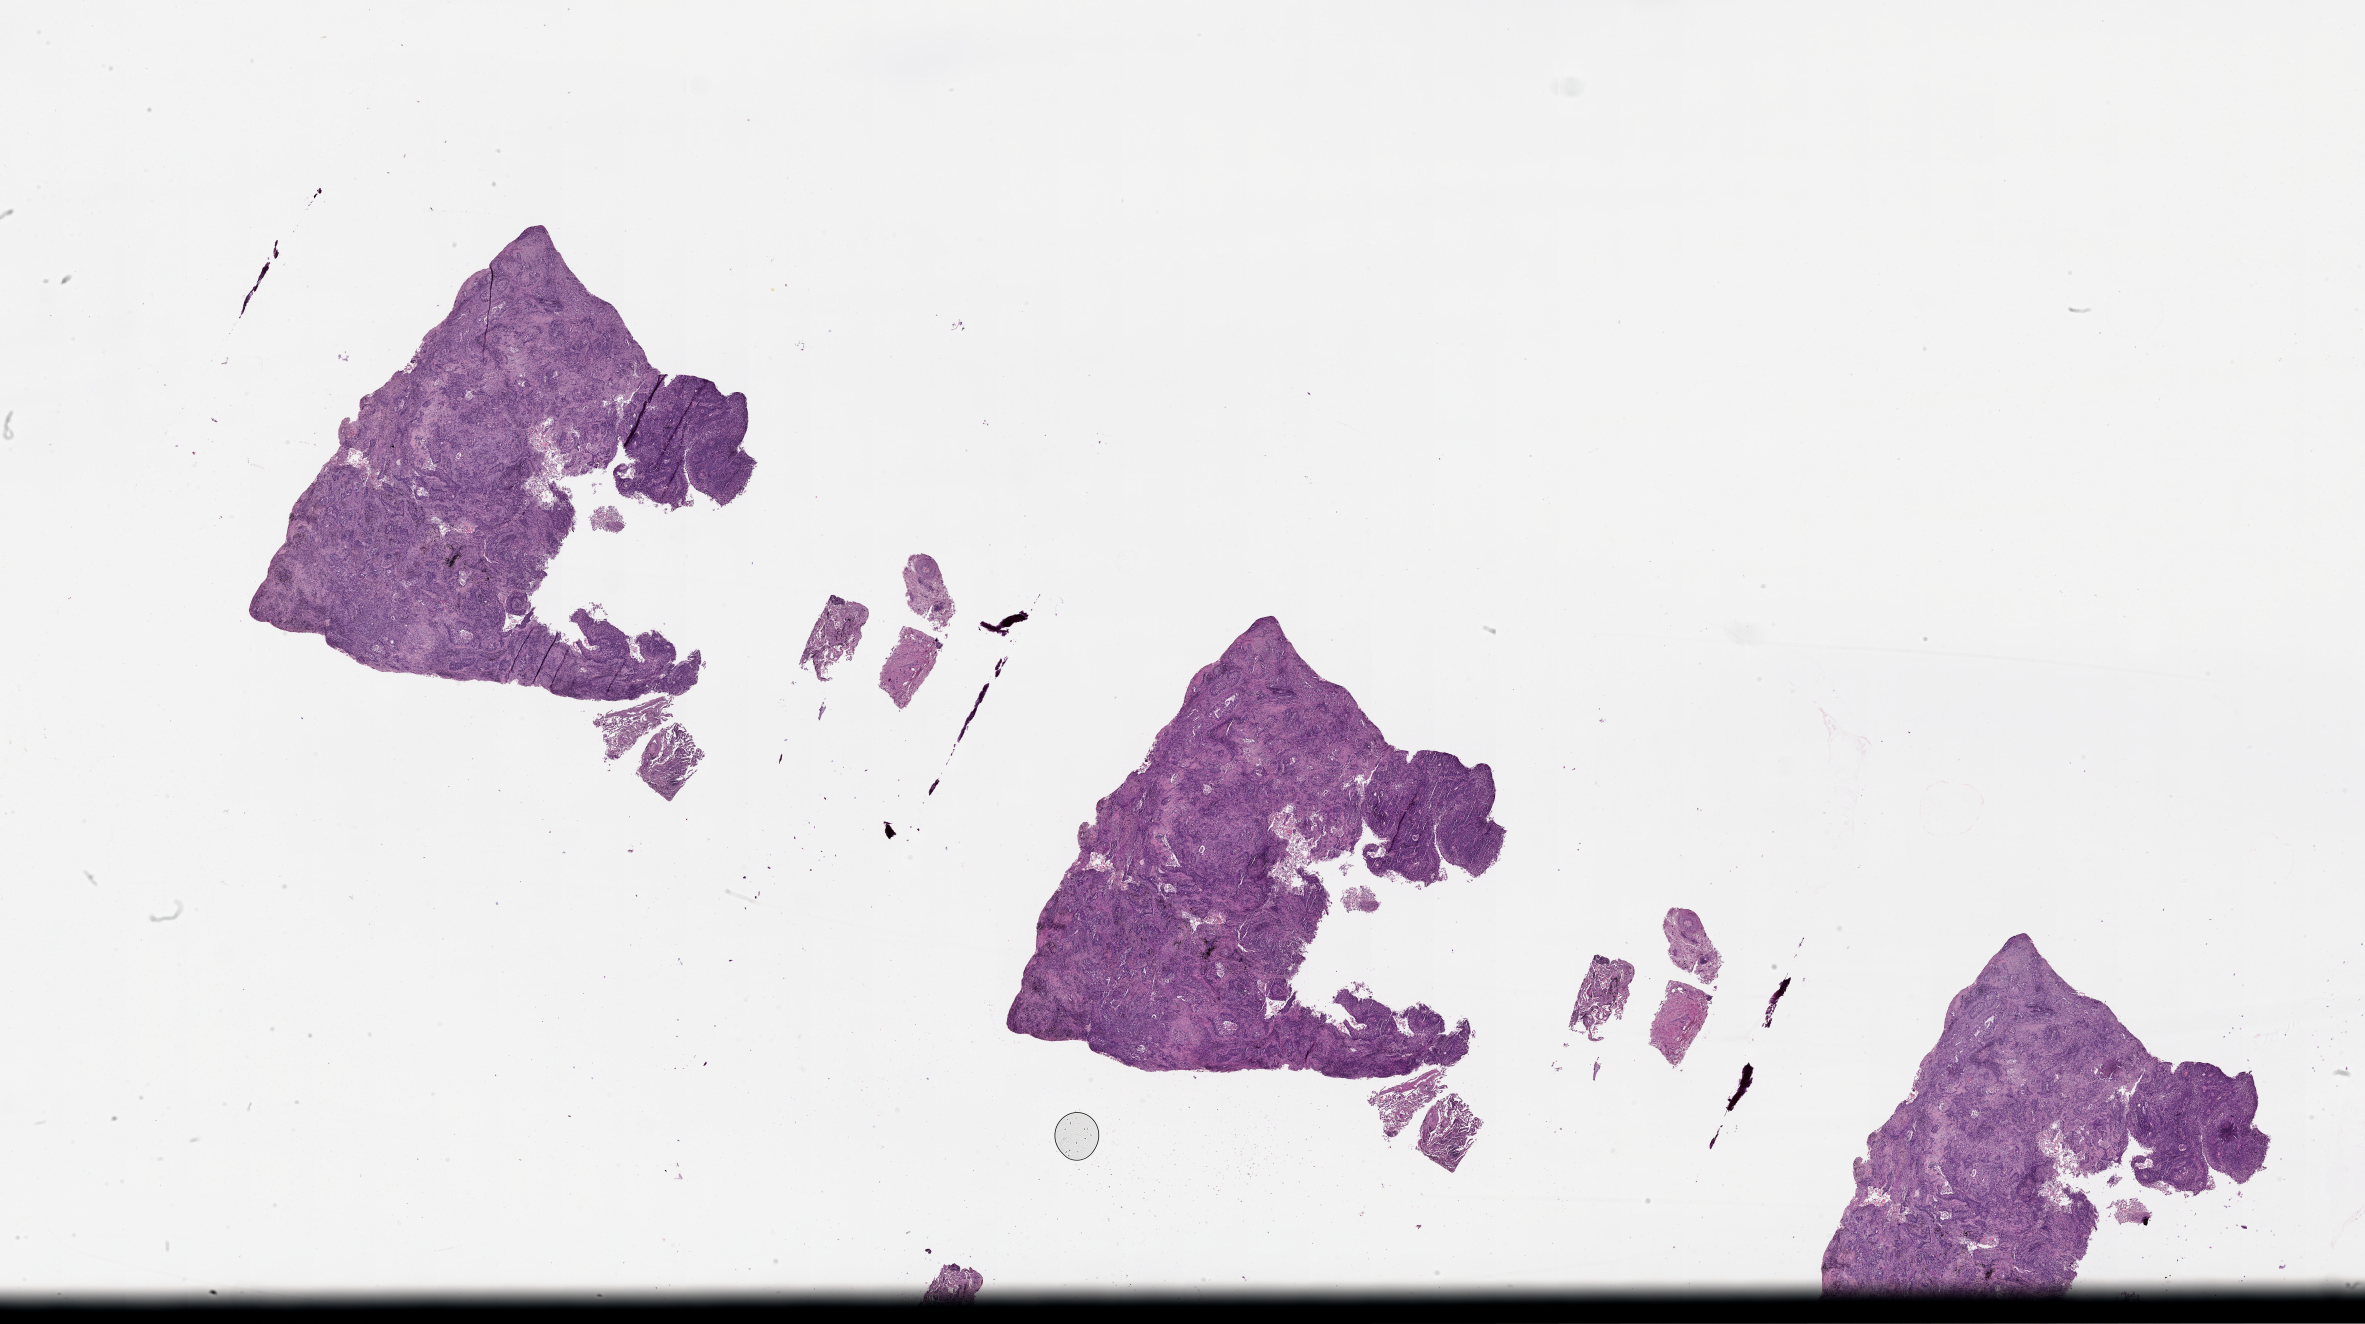
Digitized H&E tissue section (whole slide), whole scanned area (about 38.1 x 21.3 mm, from a 20x scan) shown as a low-resolution overview. Tumour tissue sample, lung. Male, 66 y/o.
Patient diagnosis (cohort enrolment): squamous cell carcinoma (lung).